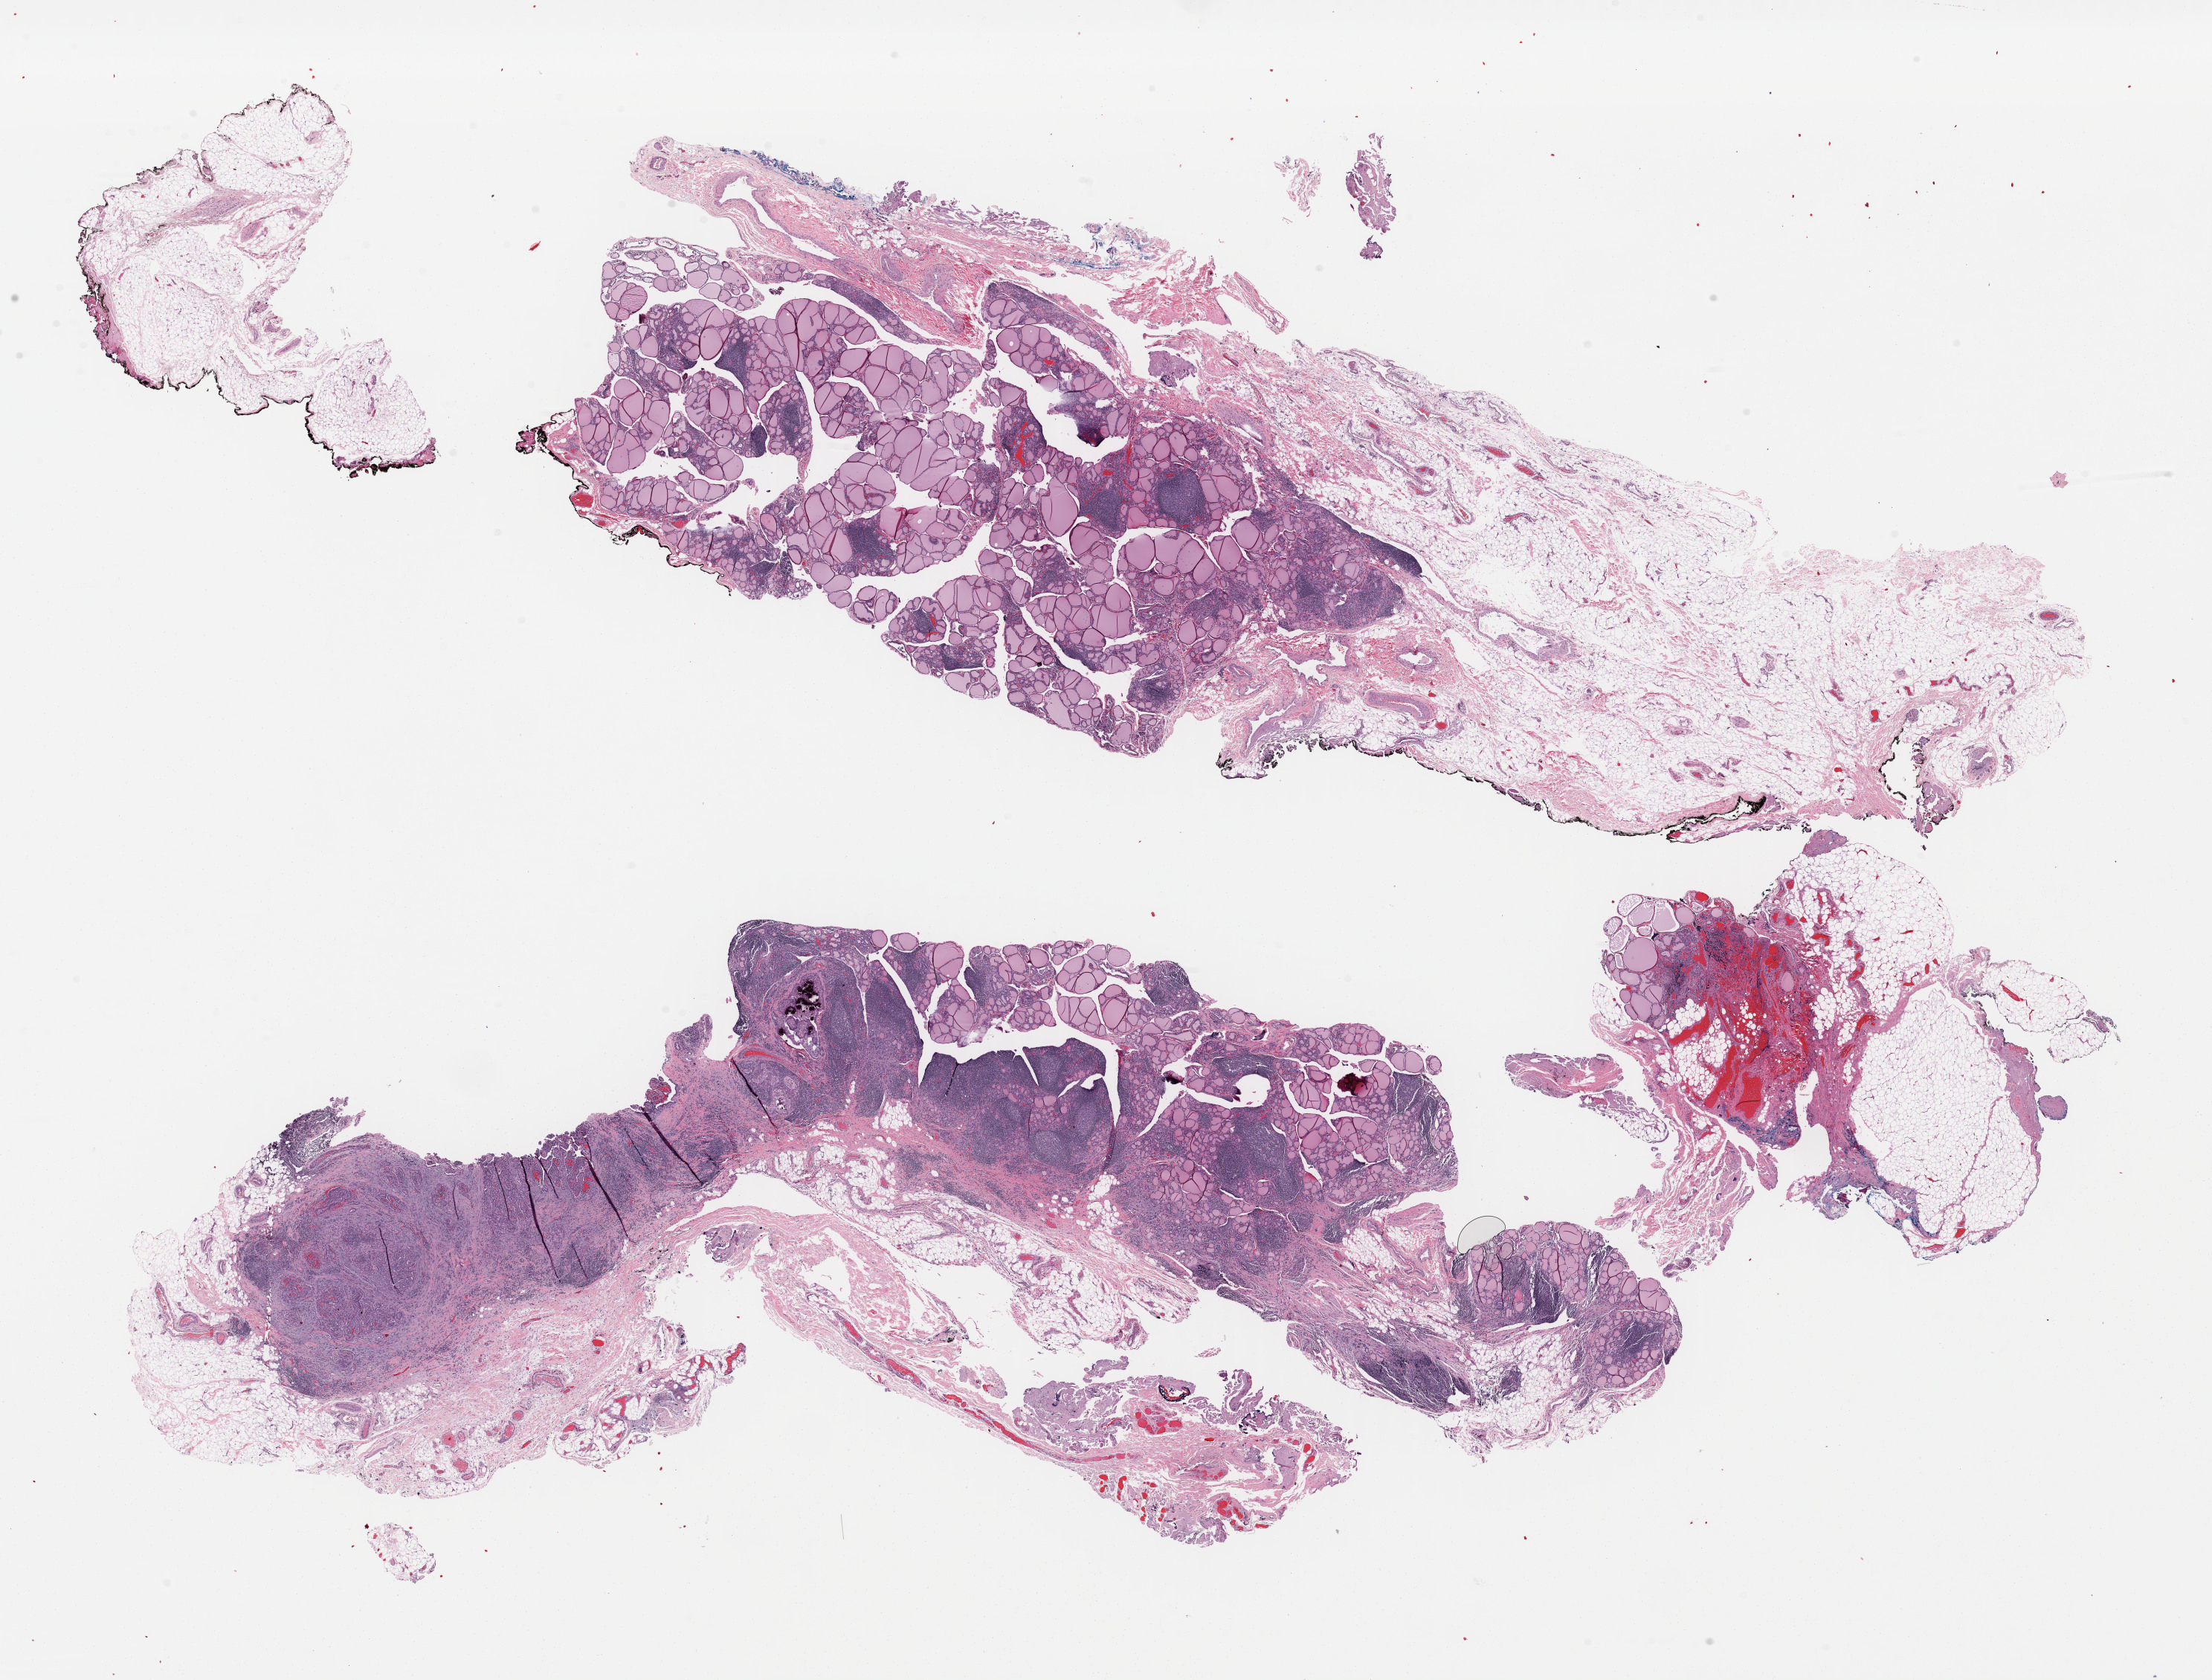
Digitized Hematoxylin and eosin (H&E) stained tissue section (whole slide), whole scanned area (about 23.5 x 17.8 mm, acquisition: 40x scan) shown as a low-resolution overview; FFPE section; thyroid, primary tumour sample. Female patient; age at initial diagnosis 32 years.
Pathologic diagnosis: Papillary adenocarcinoma, NOS (thyroid gland). Lymph nodes positive (case pathology): 6 of 14 examined. AJCC pathologic stage: I (7th edition).